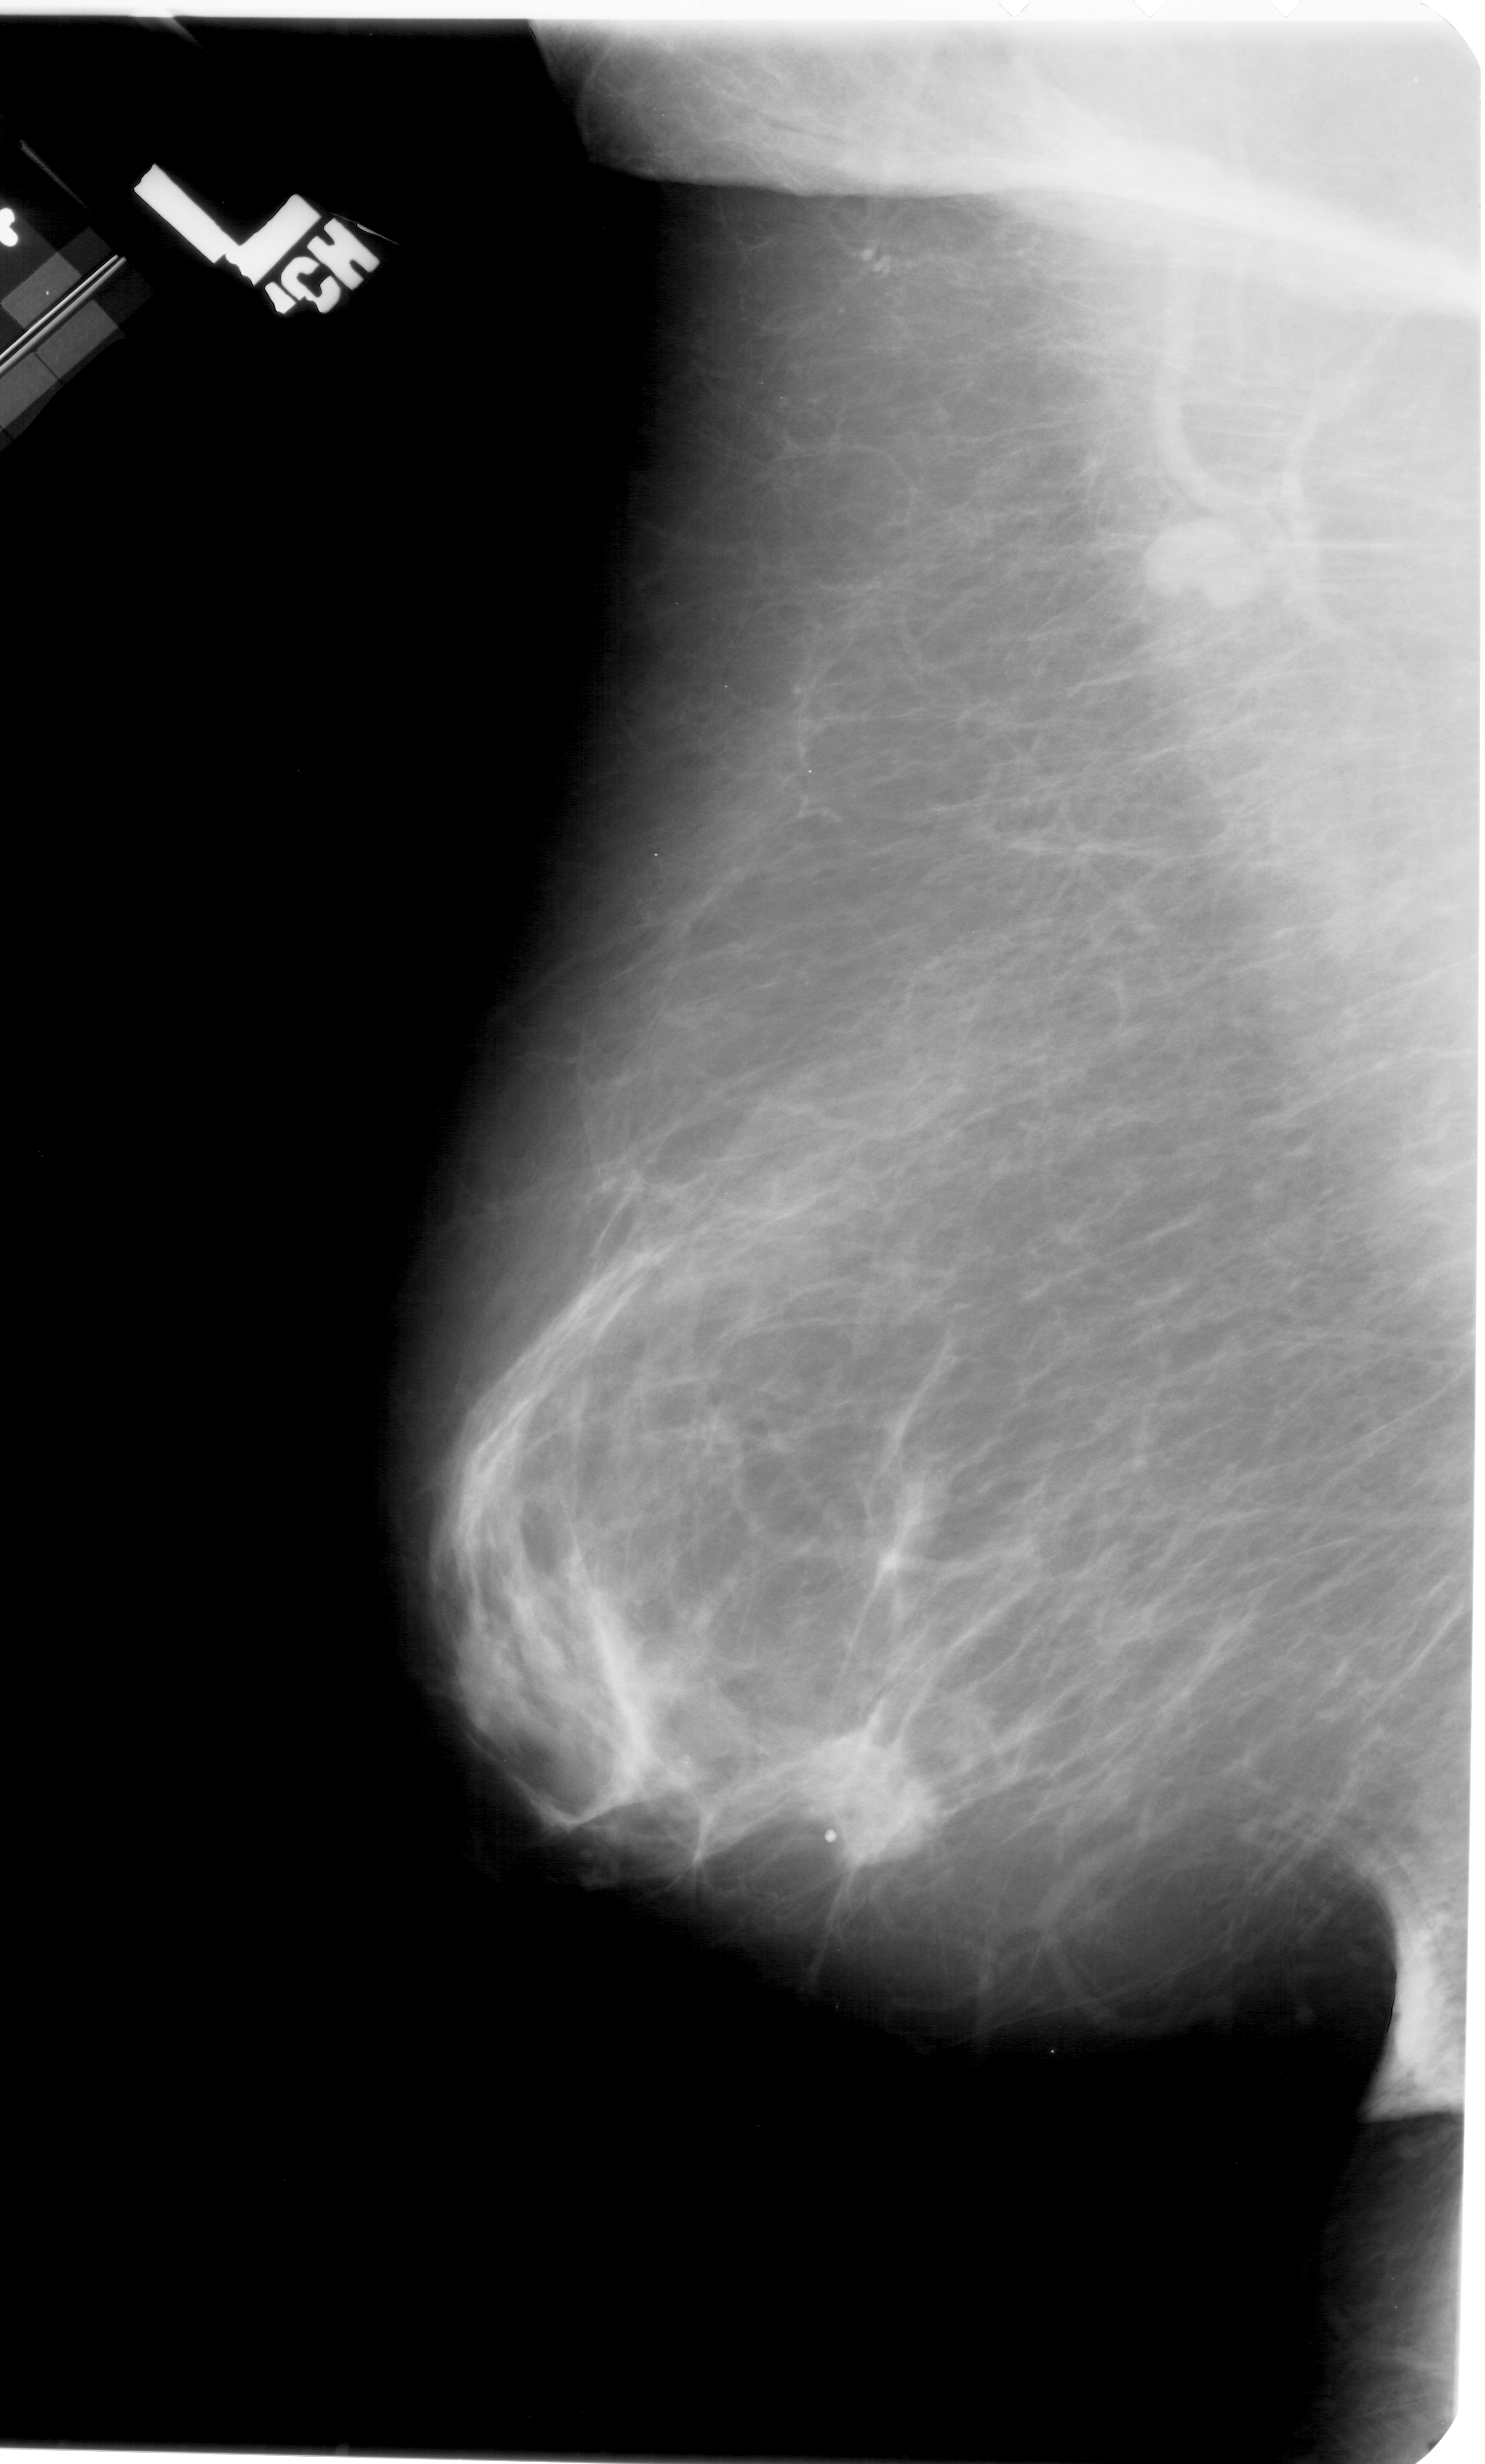
Digitized screen-film mammogram; left breast; MLO view; BI-RADS breast density category 1 (scale 1–4).
Marked findings (only marked abnormalities are described; nothing is implied about the rest of the image): mass, shape oval, margins spiculated; BI-RADS assessment category 5; subtlety rating 5 on a 1 (subtle) to 5 (obvious) scale; pathology (as recorded): malignant.